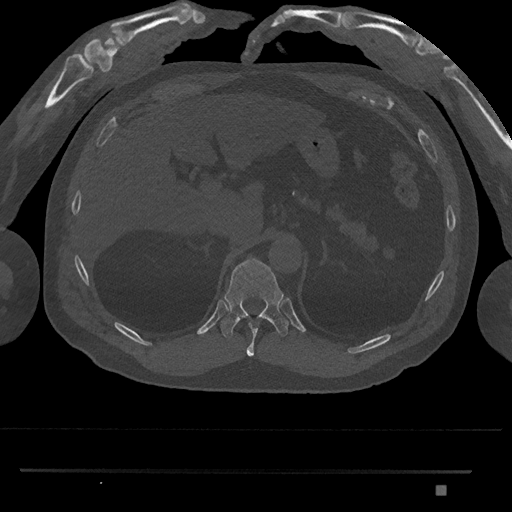
CT including the spine, one axial slice. Bone window (W 1800 / L 400 HU). 512 × 512 image matrix, field of view 429 × 429 mm. Male patient, age 65 years. Case-level facts recorded for this patient, not image findings: primary cancer: prostate.
Structures marked on this image (semi-automatic segmentation, software-assisted and operator-edited):
- T10 vertebra: box from (x=246, y=323) to (x=258, y=357) px
- T11 vertebra: (x=220, y=258)–(x=289, y=339)